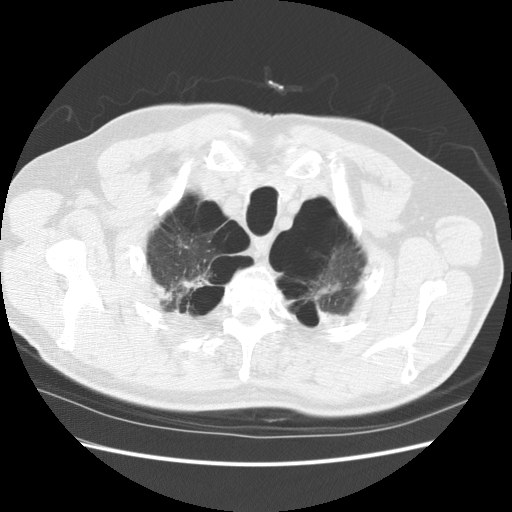
Axial slice from a low-dose chest CT screening exam; first (baseline) screen; lung window (W 1500 / L -600 HU); 2.5 mm slice thickness; standard (soft-tissue) reconstruction kernel (STANDARD). Male, age 68 years at enrolment.
Expert-annotated lung lesion, bounding box (x1, y1, x2, y2) in pixels: (142, 262, 217, 326). The screening reader recorded 2 non-calcified nodules or masses ≥4 mm on this exam; which of them this box marks is not recorded. Participant outcome: lung cancer diagnosed 1003 days after this screen (after the third annual screen) — large cell carcinoma, NOS, right upper lobe, poorly differentiated (G3), stage IV (AJCC 6th edition).